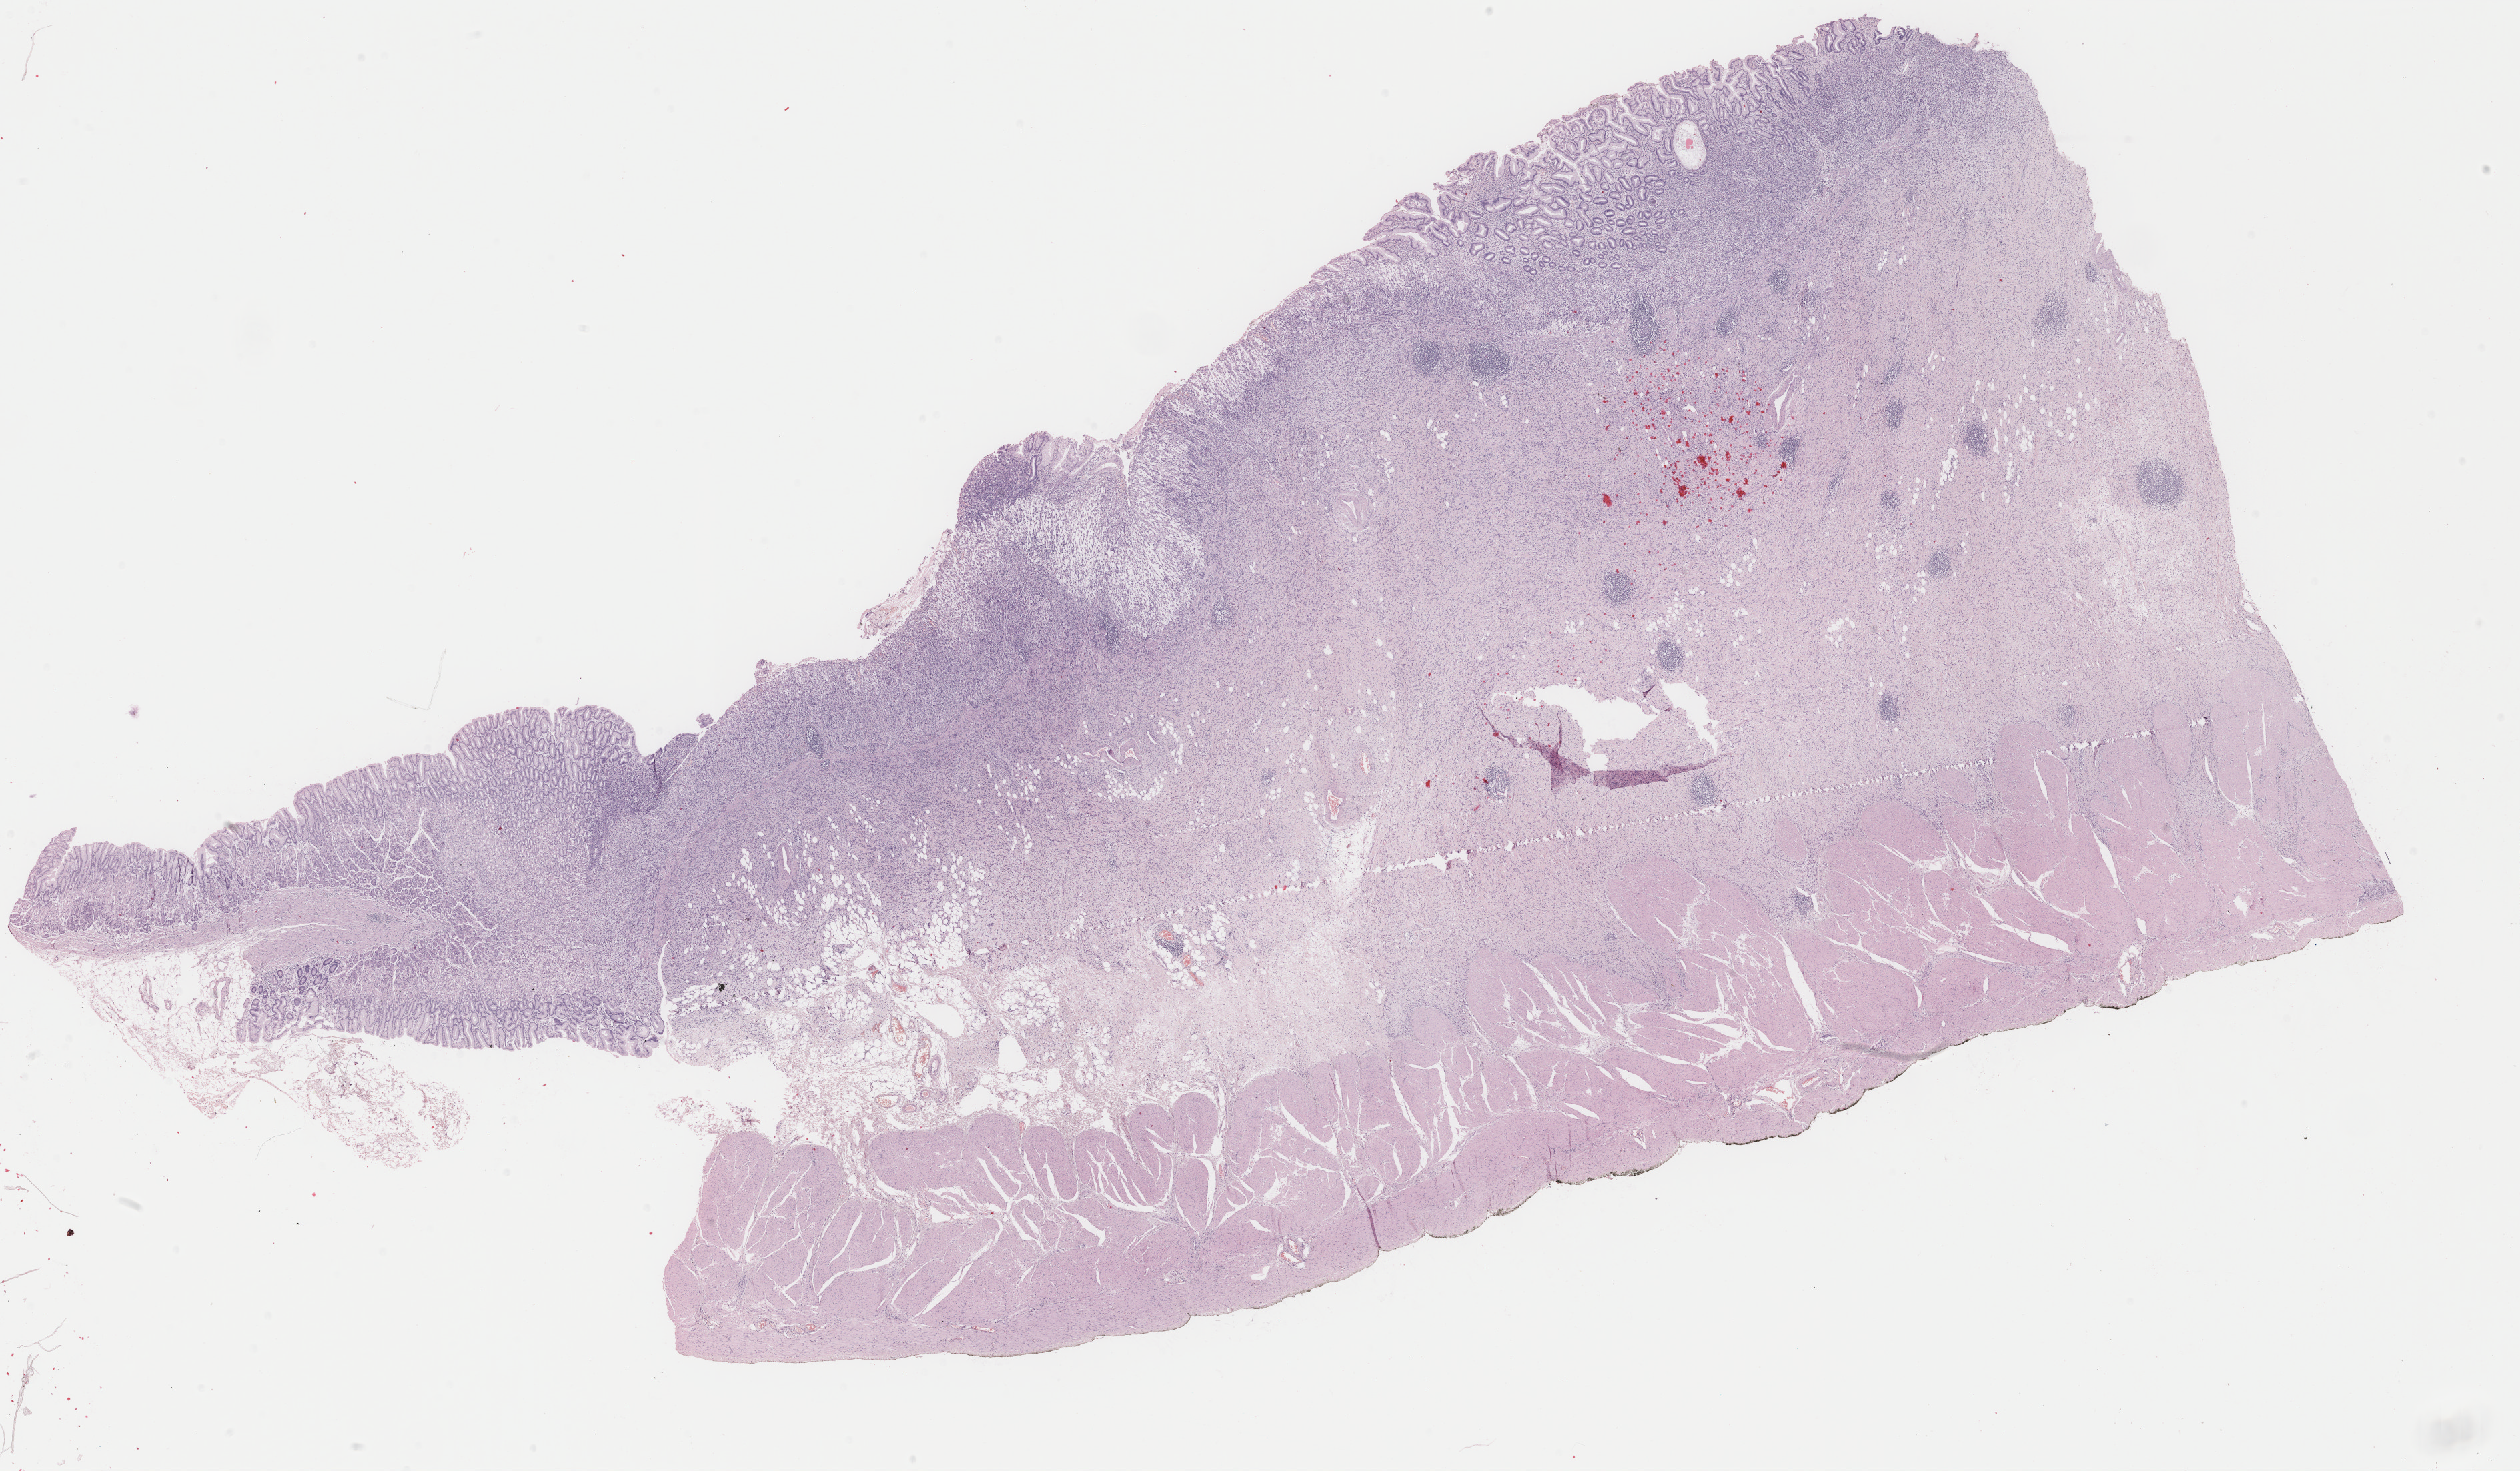
Whole-slide histology image, Hematoxylin and eosin (H&E) stained, whole scanned area (about 30.0 x 17.5 mm) shown as a low-resolution overview, formalin-fixed paraffin-embedded (FFPE) diagnostic section, primary tumour sample from the stomach. Male patient; age at initial diagnosis 72 years. Histologic grade: G3 (poorly differentiated).
- TNM: T2 N3a M0
- diagnosis: Adenocarcinoma, NOS (gastric antrum)
- AJCC pathologic stage: IIIA
- lymph nodes positive (case pathology): 13 of 16 examined